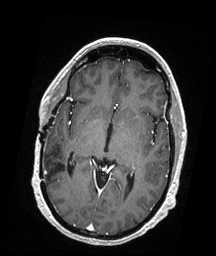
Brain MRI from a brain-tumour surgery series, one axial slice; slice 98 of 176 in the series (ordered by position); T1-weighted post-contrast; 1 mm slice thickness; 216 × 256 image matrix, field of view 211 × 250 mm. From the clinical record (not read from this slice): histopathology: Demyelinating Lesions (Multiple Sclerosis Plaques); tumour location: Left Occipital.
Outlined on this slice (expert manual segmentation):
- tumour: bounding box (x1, y1, x2, y2) in pixels: (122, 209, 127, 212)